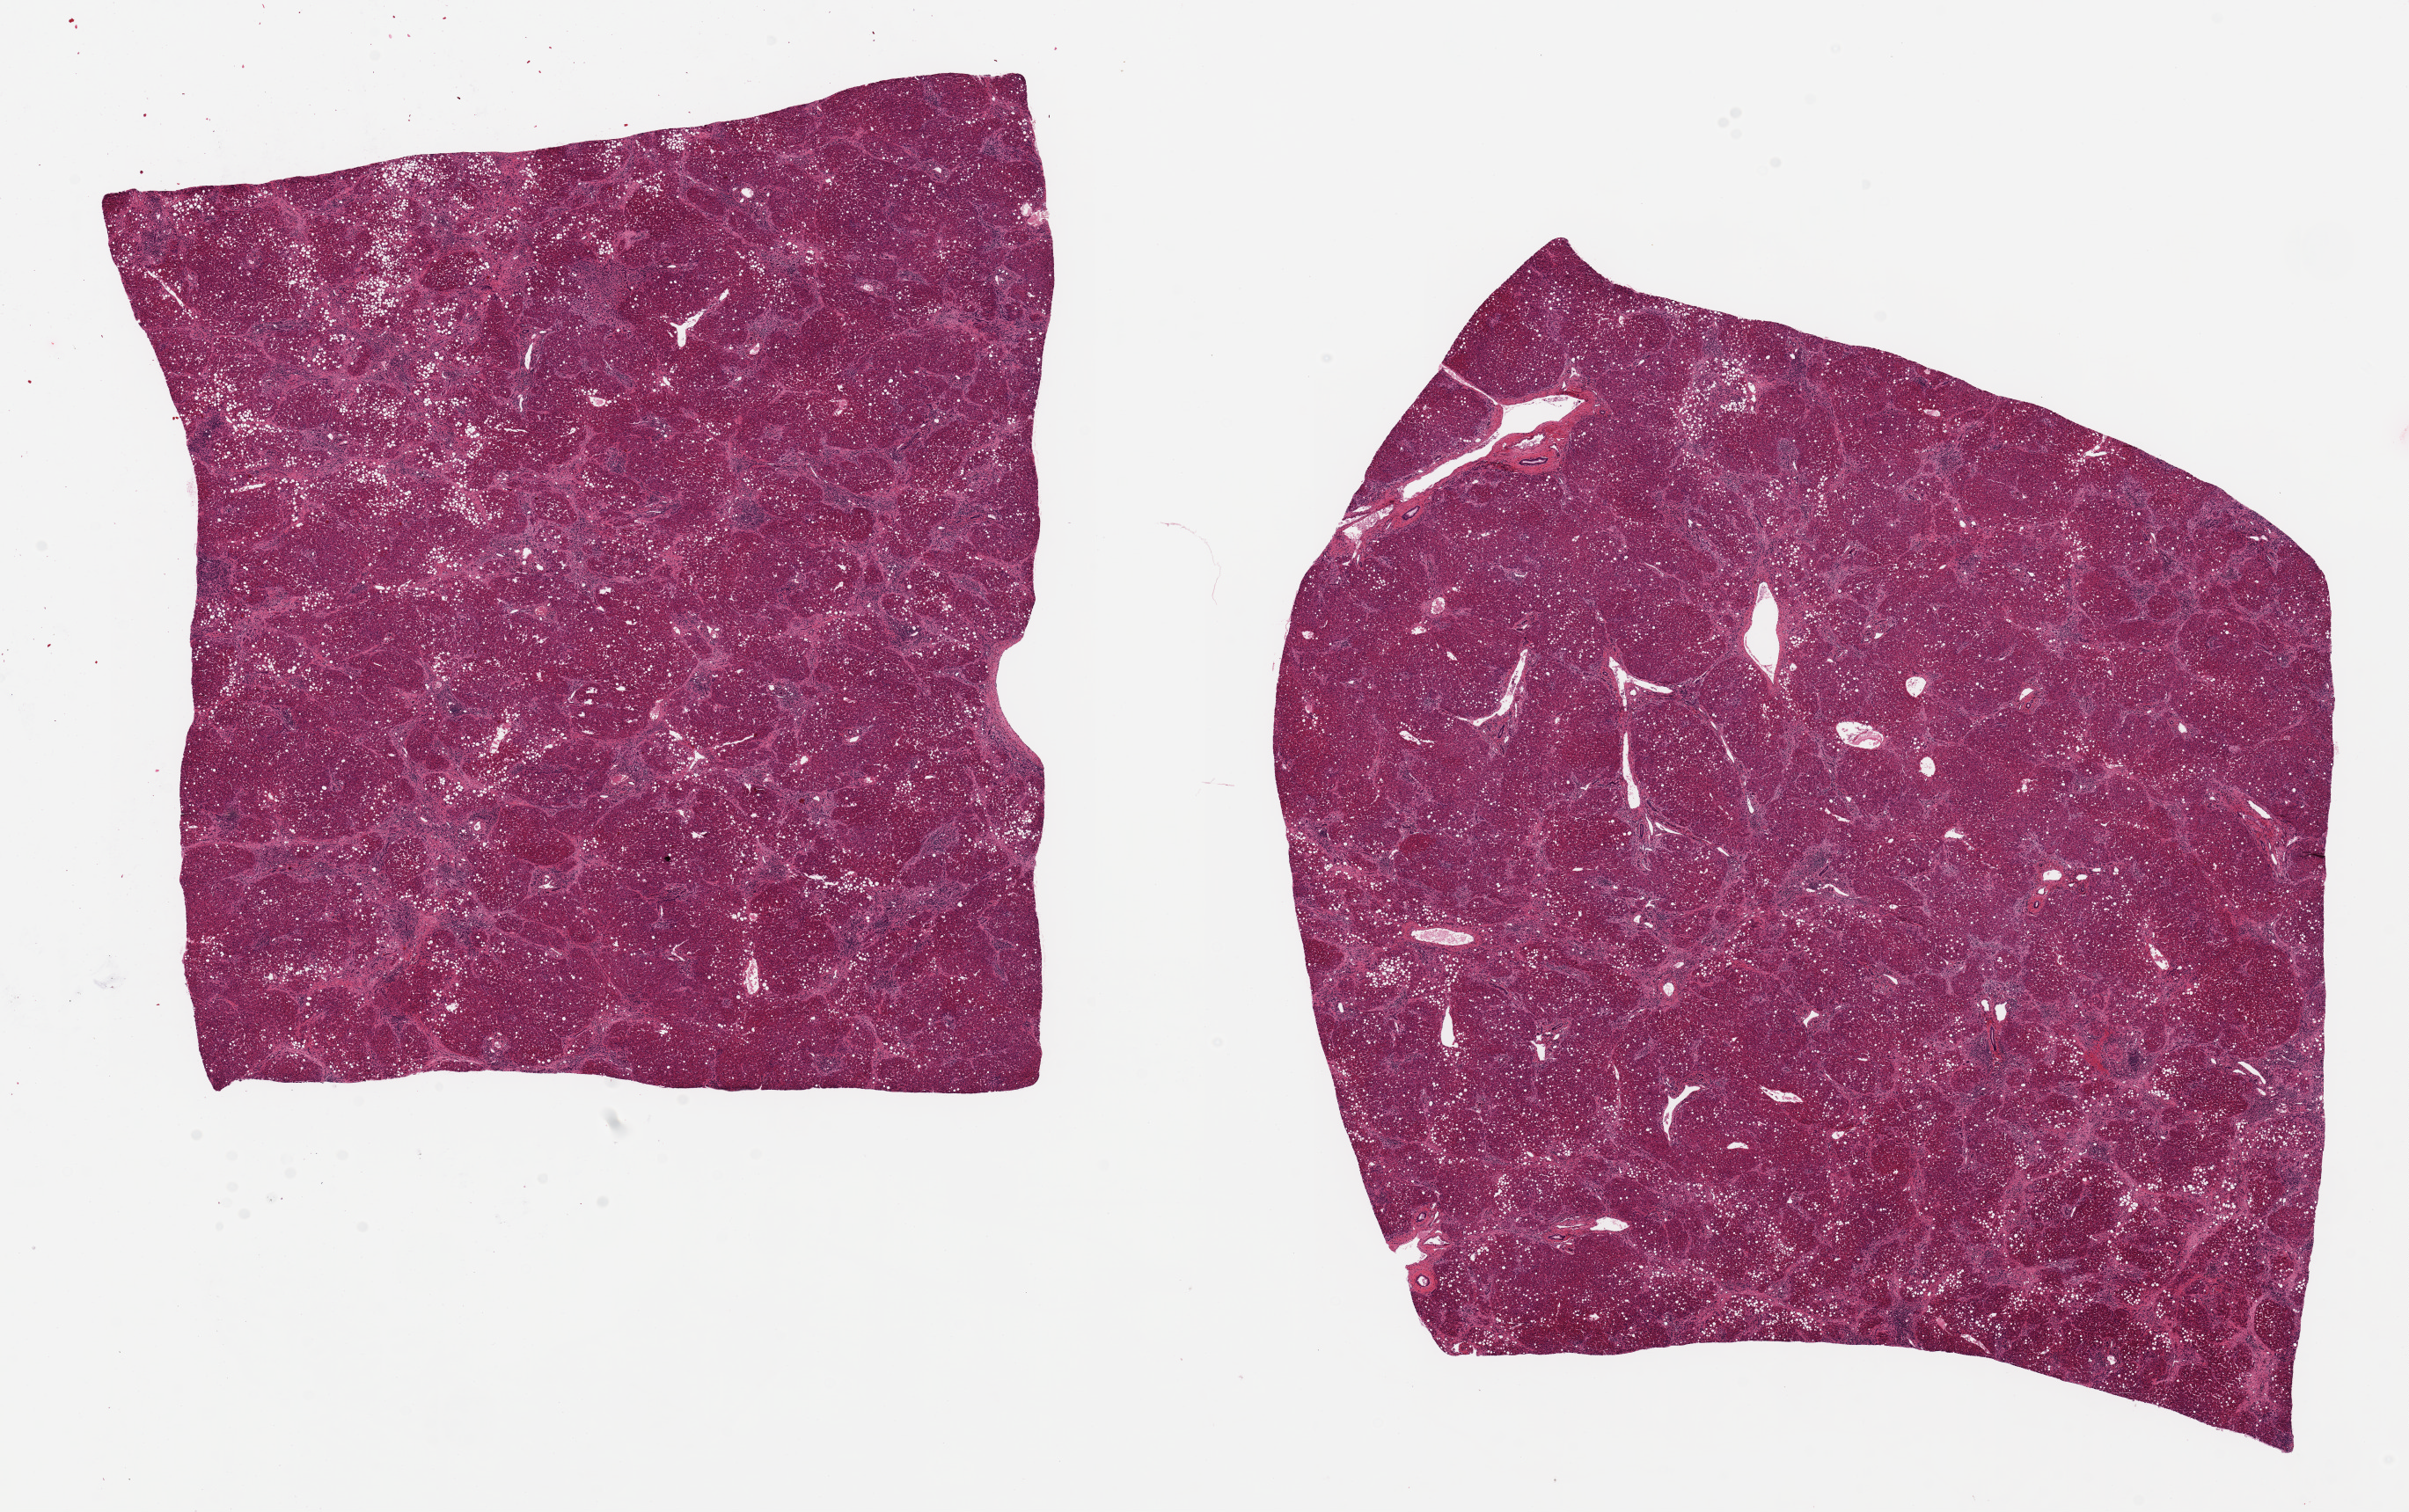
Digitized hematoxylin and eosin (H&E)-stained section, shown as a low-resolution overview of the whole scanned area (about 21.7 x 13.6 mm, from a 20x scan), PAXgene-fixed, paraffin-embedded tissue, sampled site (target tissue): liver, donor tissue sample. Donor: male.
Pathologist's review note for this sample: 2 ~9.5x8mm aliquots. Macrovesicular steatohepatitis (~20% fat), bridging fibrosis focally approaching early cirrhosis; moderate chronic inflammation.